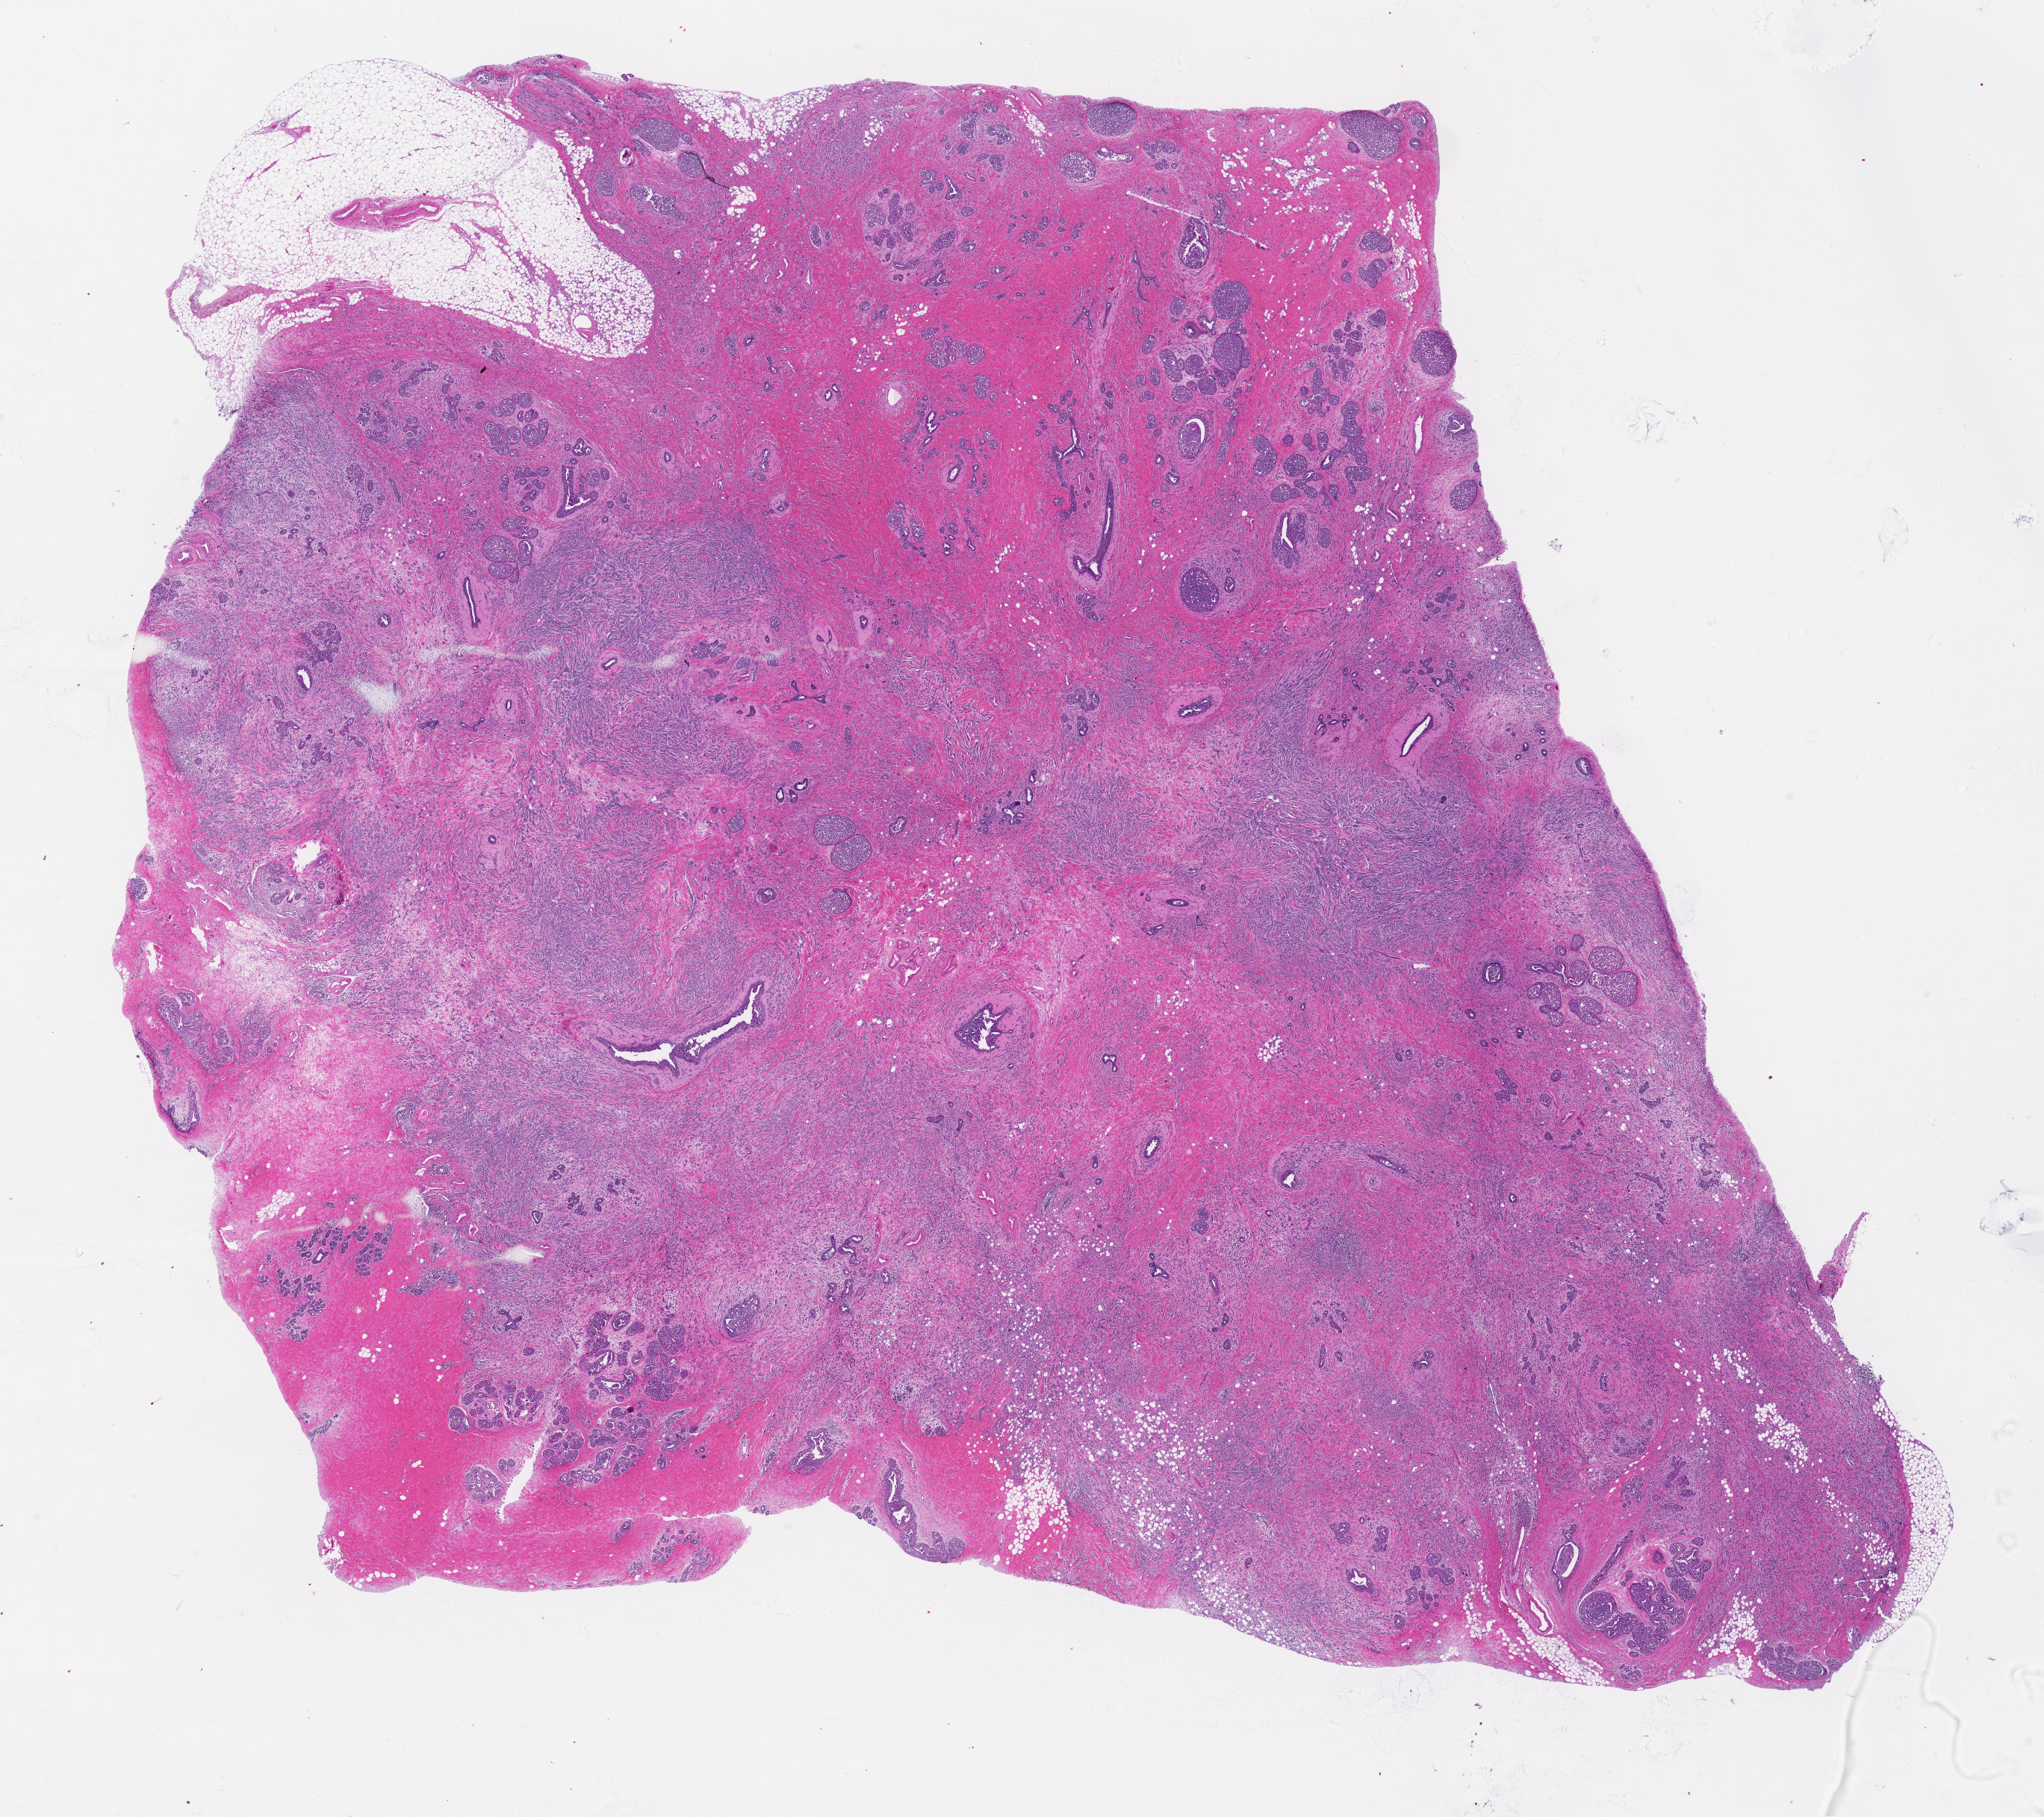
Digitized H&E-stained tissue section (whole slide) — shown as a low-resolution overview of the whole scanned area (about 21.6 x 19.2 mm, acquisition: 40x scan). FFPE section. Sample: primary tumour, breast. Female, age 44 years at initial diagnosis.
AJCC pathologic stage: IIA (6th edition). Laterality: left. Diagnosis: Lobular carcinoma, NOS. TNM: T2 N0 (i-) M0. Lymph nodes positive (case pathology): 0 of 14 examined.